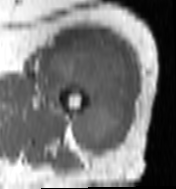
MRI of an extremity soft-tissue mass, one axial slice; slice 78 of 100 in the series (ordered by position); MR volume resampled by the dataset authors to the PET/CT grid (not the native acquisition matrix); 3.27 mm slice thickness; 176 × 189 image matrix. Female patient. Case-level facts recorded for this patient, not image findings: histological type: undifferentiated – high grade; grade: high; site of the primary tumour: left thigh.
Structures marked on this image (expert contour drawn on MRI and transferred to this co-registered scan by the dataset authors):
- gross tumour volume including surrounding oedema: bounding box <46,41,129,158> (left, top, right, bottom; pixels)
- gross tumour volume (mass): <48,50,127,156>